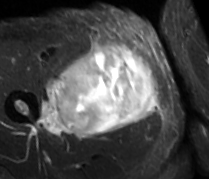
MRI of an extremity soft-tissue mass, one axial slice. Position 39 of 89 along the scan axis. STIR. MR volume resampled by the dataset authors to the PET/CT grid (not the native acquisition matrix). 209 × 179 image matrix. Male patient. From the clinical record (not read from this slice): histological type: undifferentiated - pleiomorphic; grade: high; site of the primary tumour: right thigh.
Structures marked on this image (expert contour drawn on MRI and transferred to this co-registered scan by the dataset authors):
- gross tumour volume including surrounding oedema: box from (x=37, y=43) to (x=159, y=136) px
- gross tumour volume (mass): (x=57, y=44)–(x=159, y=136)